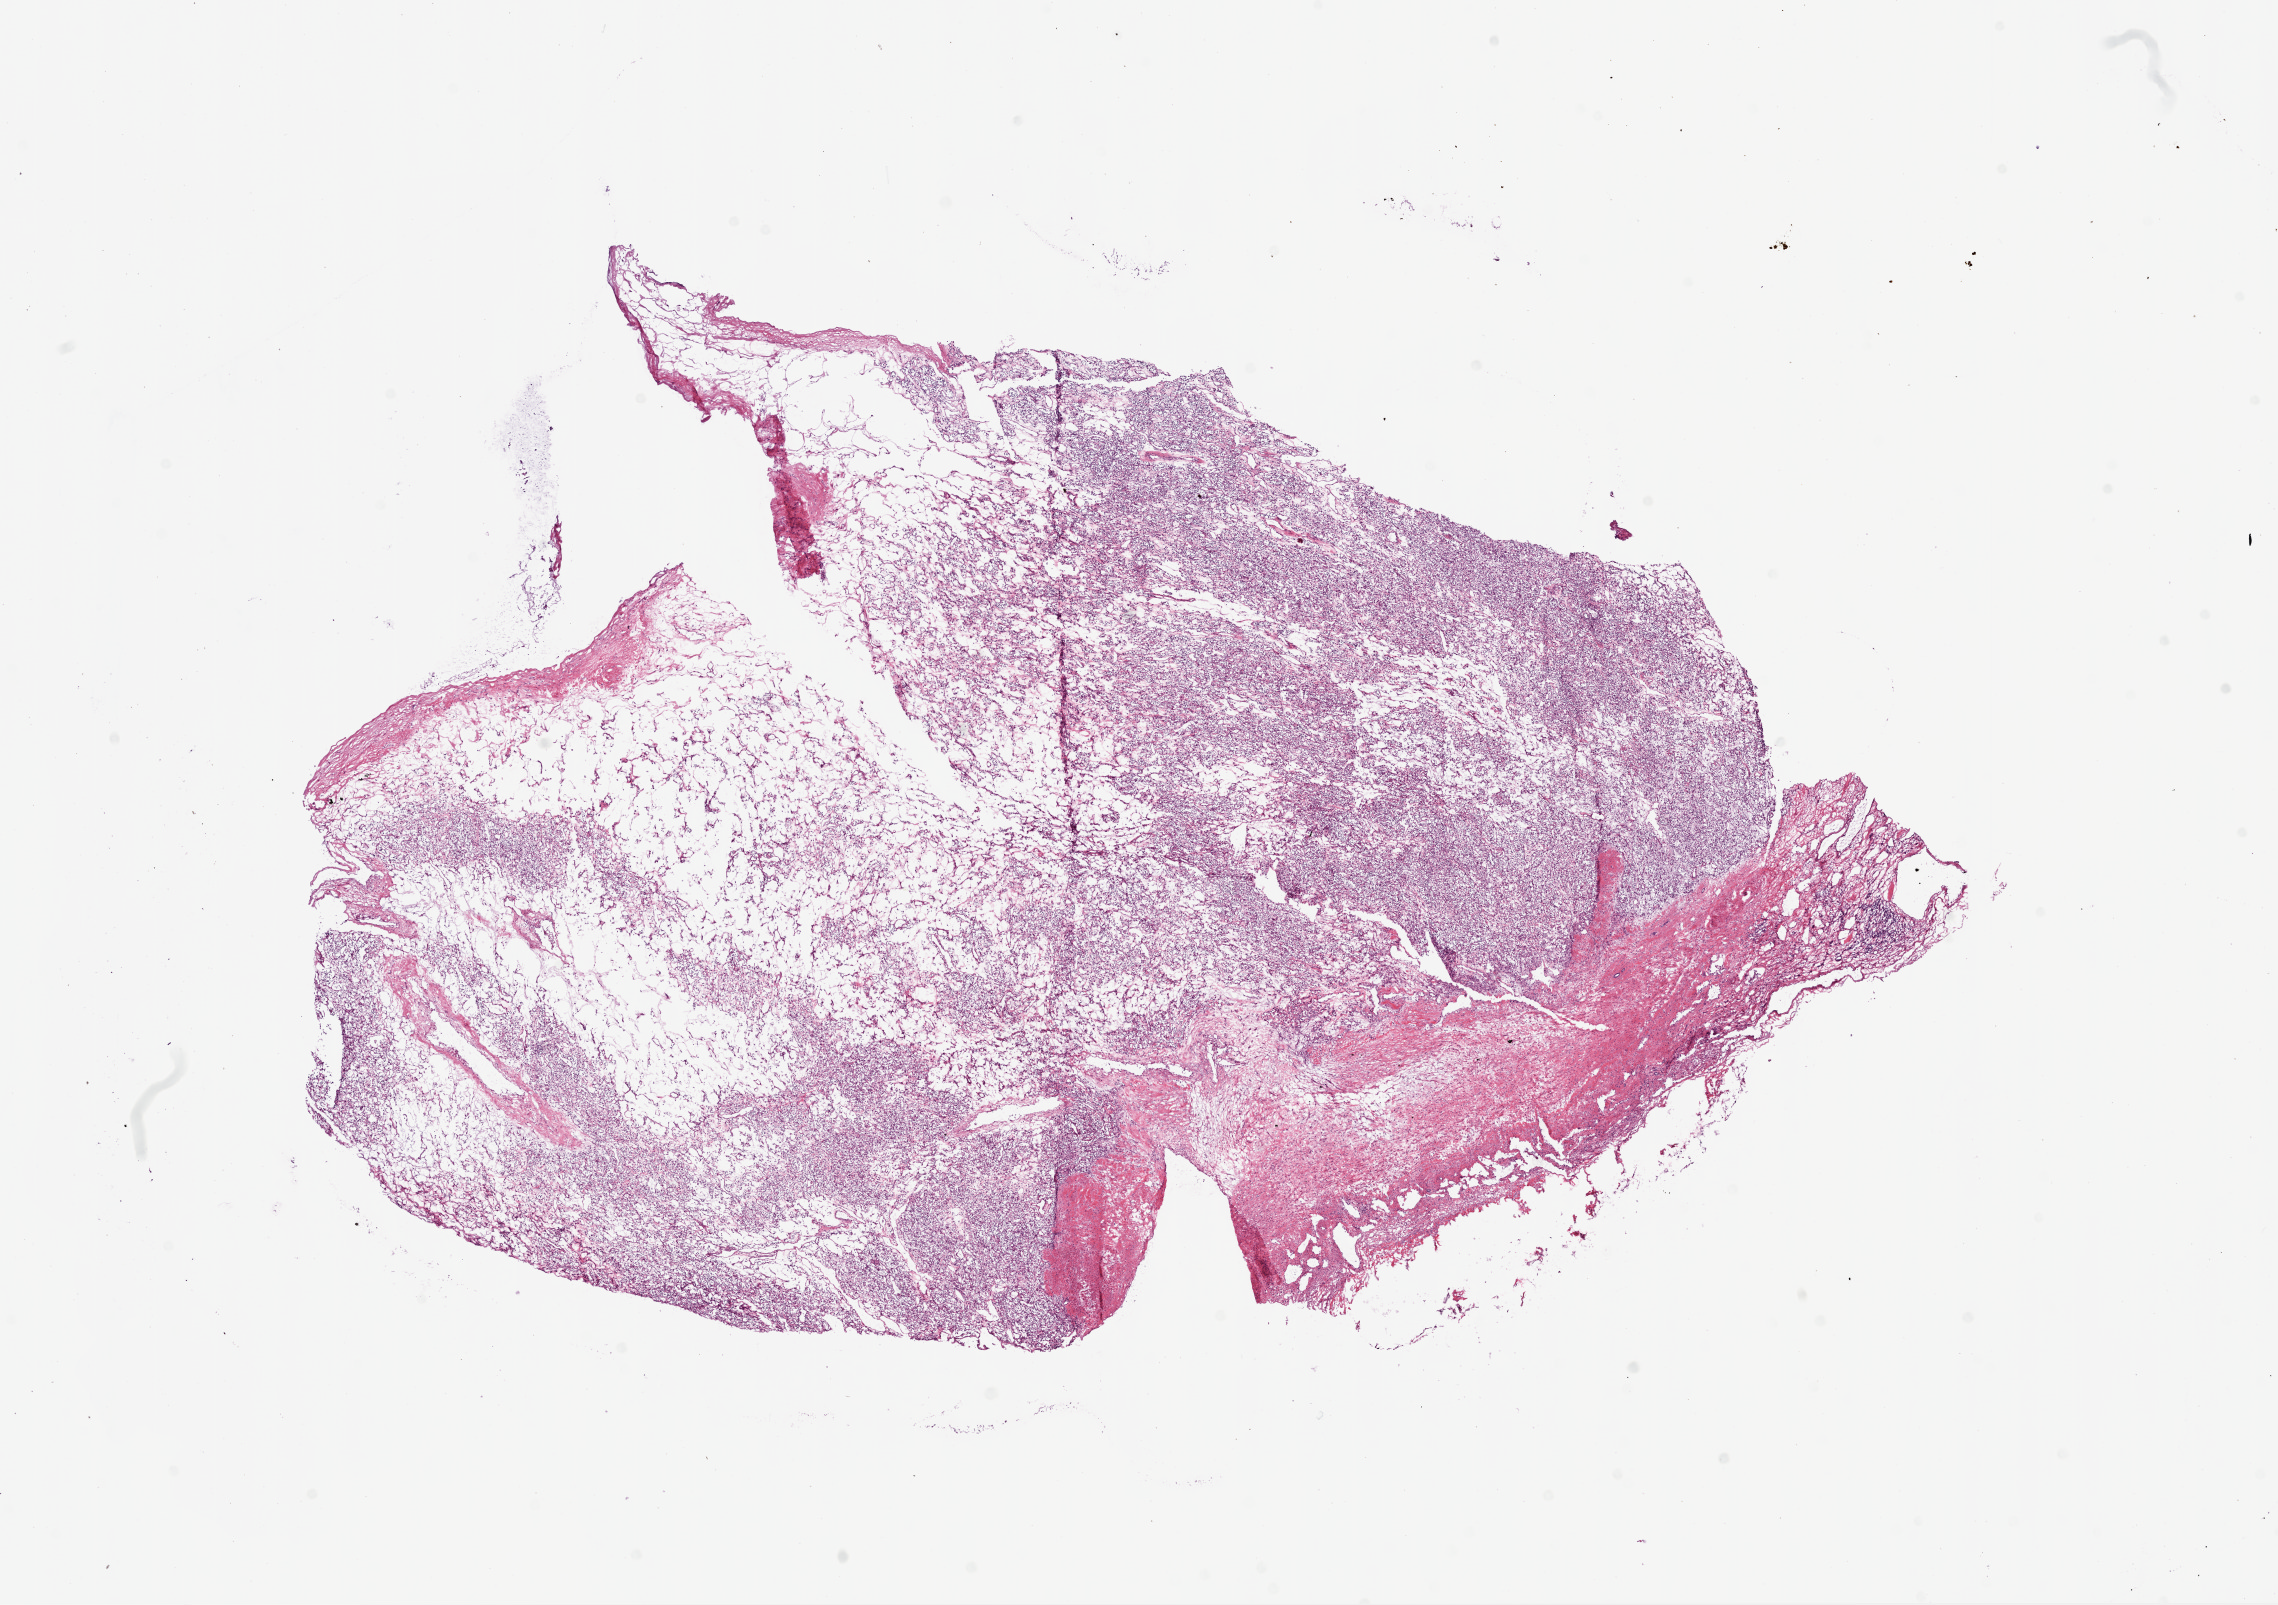
Whole-slide histology image, H&E — whole scanned area (about 18.4 x 12.9 mm, acquisition: 20x scan) shown as a low-resolution overview, frozen section from the bottom of the tissue portion, sample: primary tumour, kidney. Male patient; age at initial diagnosis 59 years. Histologic grade: G1 (well differentiated). Composition of this section per pathologist review: tumour cells 80%, tumour nuclei 80%, normal cells 0%, stromal cells 20%, necrosis 0%. Inflammatory infiltration, as recorded: lymphocyte infiltration 2%, monocyte infiltration 0%, neutrophil infiltration 0%.
- histologic diagnosis: Clear cell adenocarcinoma, NOS
- AJCC pathologic stage: I (7th edition)
- TNM: T1 N0 M0
- laterality: right